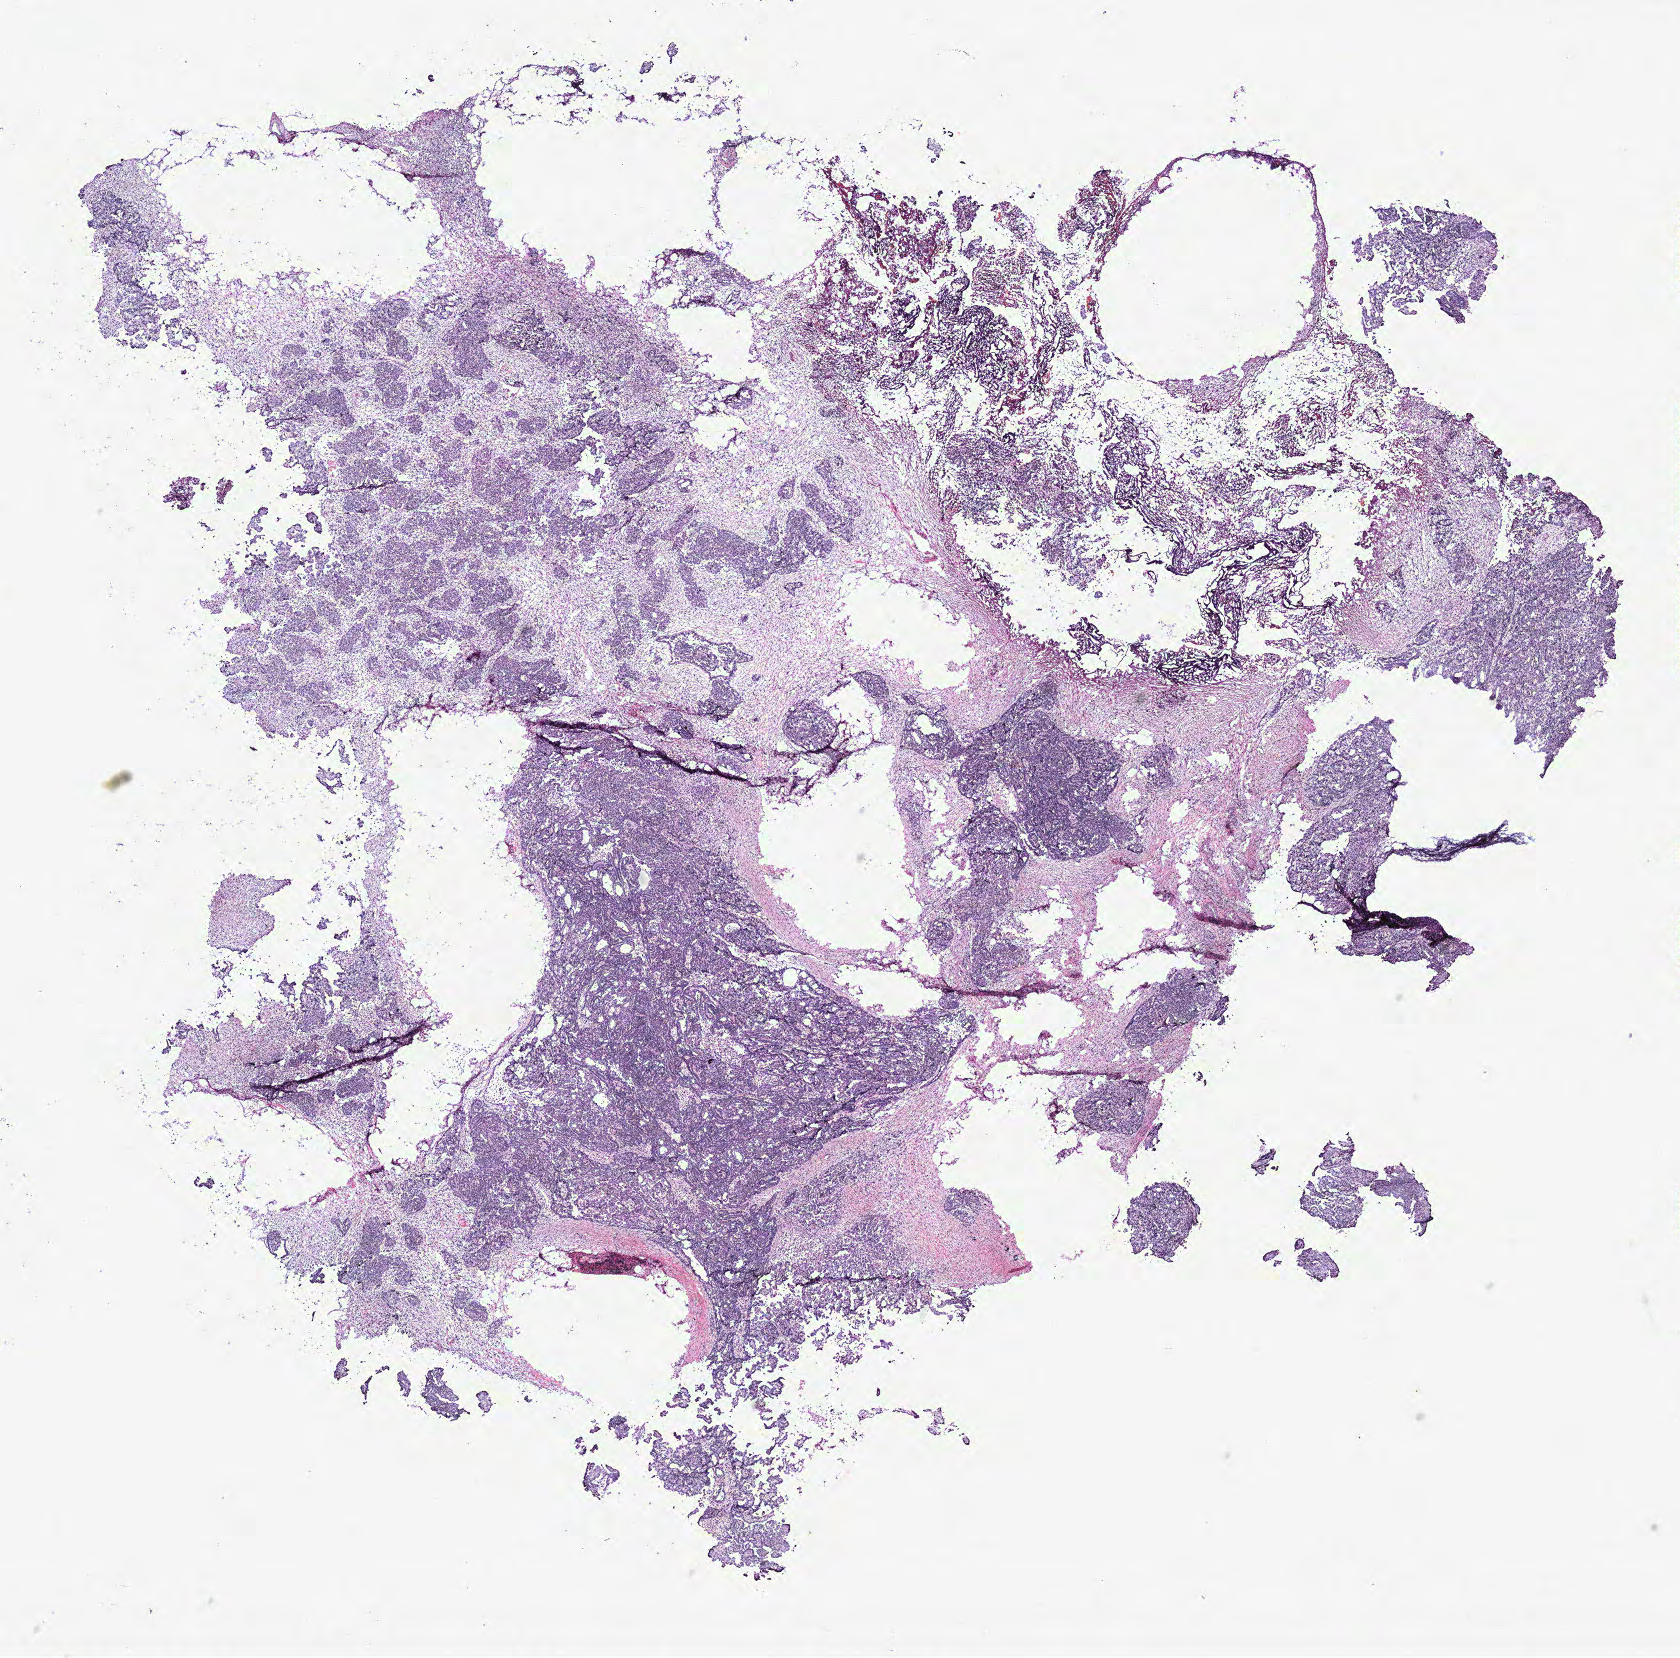
Hematoxylin and eosin (H&E) stained whole-slide image, low-resolution overview of the scanned area, about 13.4 x 13.3 mm. Tumour tissue sample, ovary. Female, 59 y/o.
* primary tumour site (as recorded): fallopian tube
* diagnosis: Serous adenocarcinoma, NOS